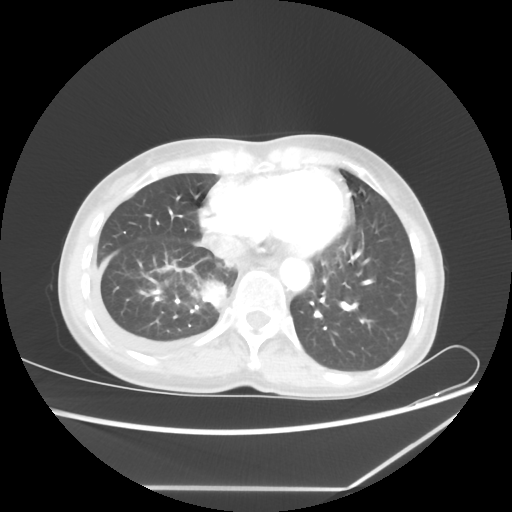
Chest CT, one axial slice; slice 18 of 60 in the series (ordered by position); reconstruction kernel STANDARD; 80 kVp; lung window (W 1500 / L -600 HU); 512 × 512 image matrix, field of view 364 × 364 mm. Female patient, age 59 years. From the clinical record (not read from this slice): clinical TNM (as recorded): T1c N1 M1.
Outlined on this slice (bounding box drawn by a radiologist):
- lung tumour (recorded histology: adenocarcinoma): box from (x=200, y=277) to (x=228, y=311) px